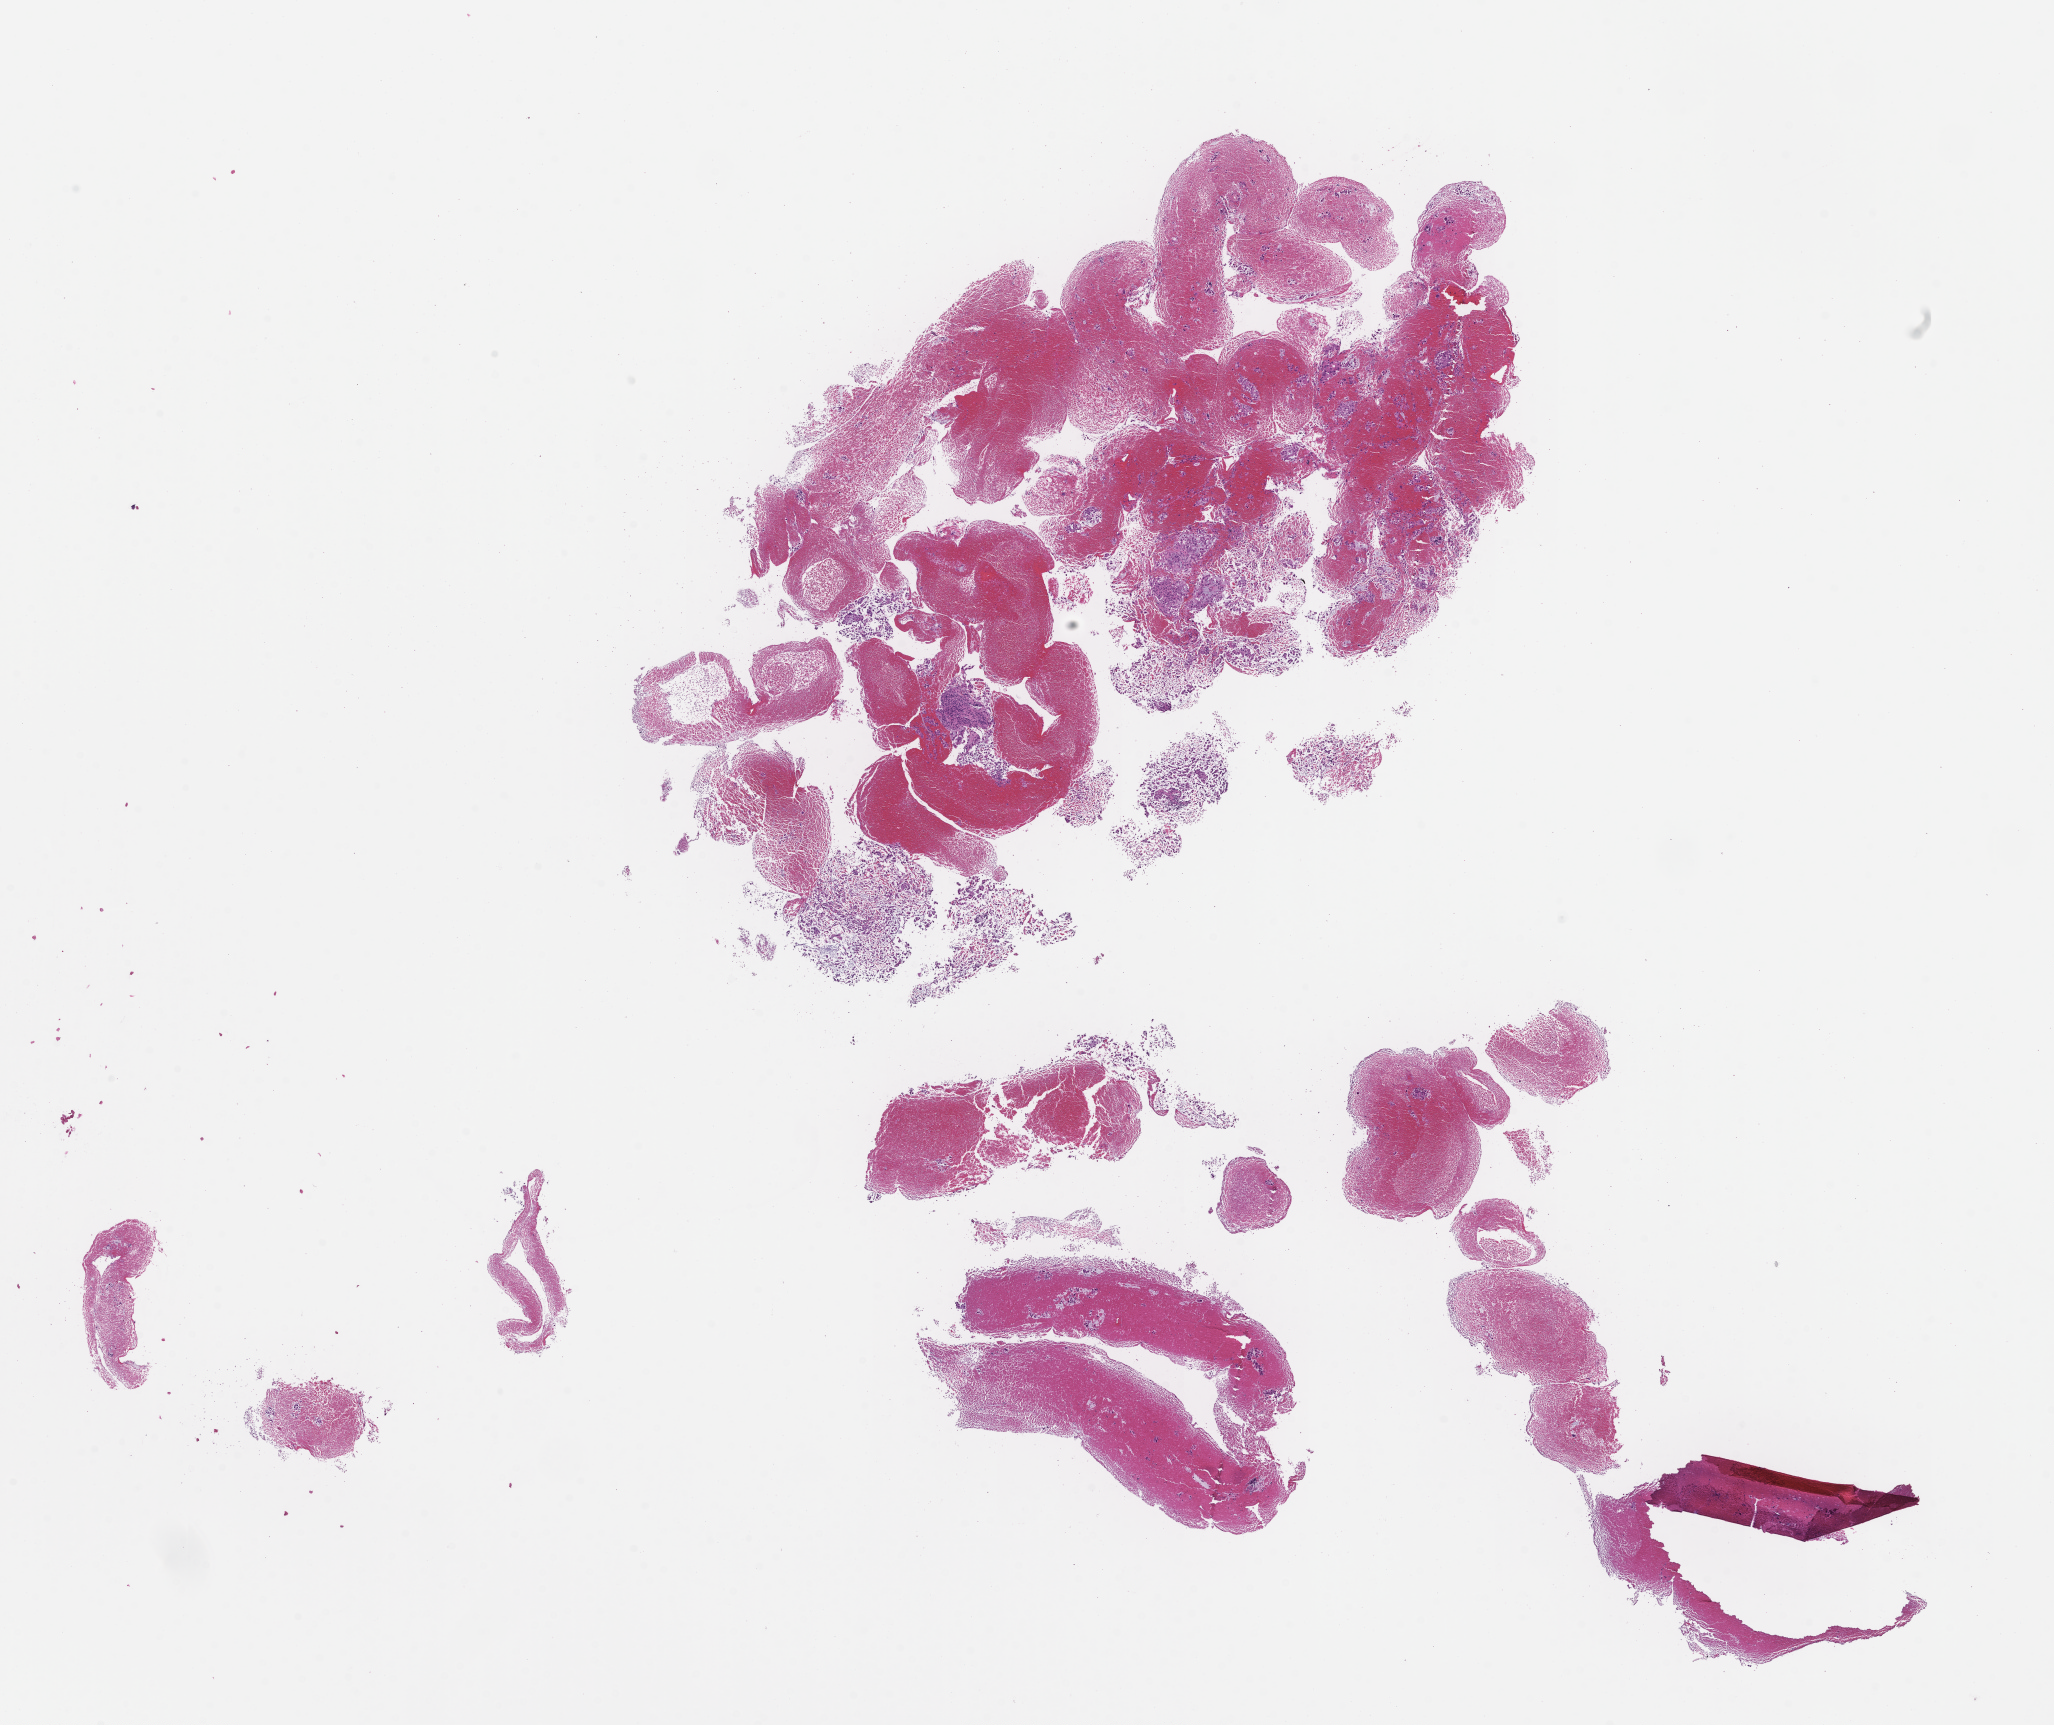
H&E whole-slide image, low-resolution overview of the scanned area, about 16.6 x 13.9 mm, formalin-fixed, paraffin-embedded (FFPE) tissue, site: lung, collected at disease progression. Patient: male.
This section: primary tumour tissue. Diagnosis: Non-Small Cell Lung Carcinoma.